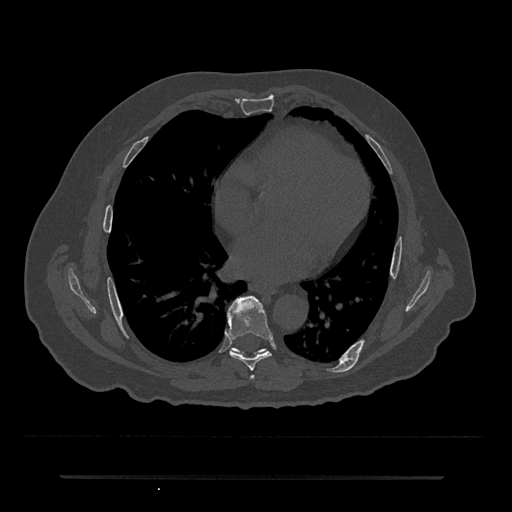
CT including the spine, one axial slice; position 372 of 797 along the scan axis; reconstruction kernel Br40s/3; 120 kVp; bone window (W 1800 / L 400 HU); 0.5 mm slice thickness; 512 × 512 image matrix, field of view 437 × 437 mm. Male patient, age 69 years. Case-level facts recorded for this patient, not image findings: primary cancer: prostate.
Annotated regions visible in this slice (semi-automatic segmentation, software-assisted and operator-edited):
- T6 vertebra: box from (x=251, y=376) to (x=254, y=379) px
- T7 vertebra: (x=227, y=295)–(x=272, y=371)
- T8 vertebra: (x=231, y=348)–(x=265, y=354)